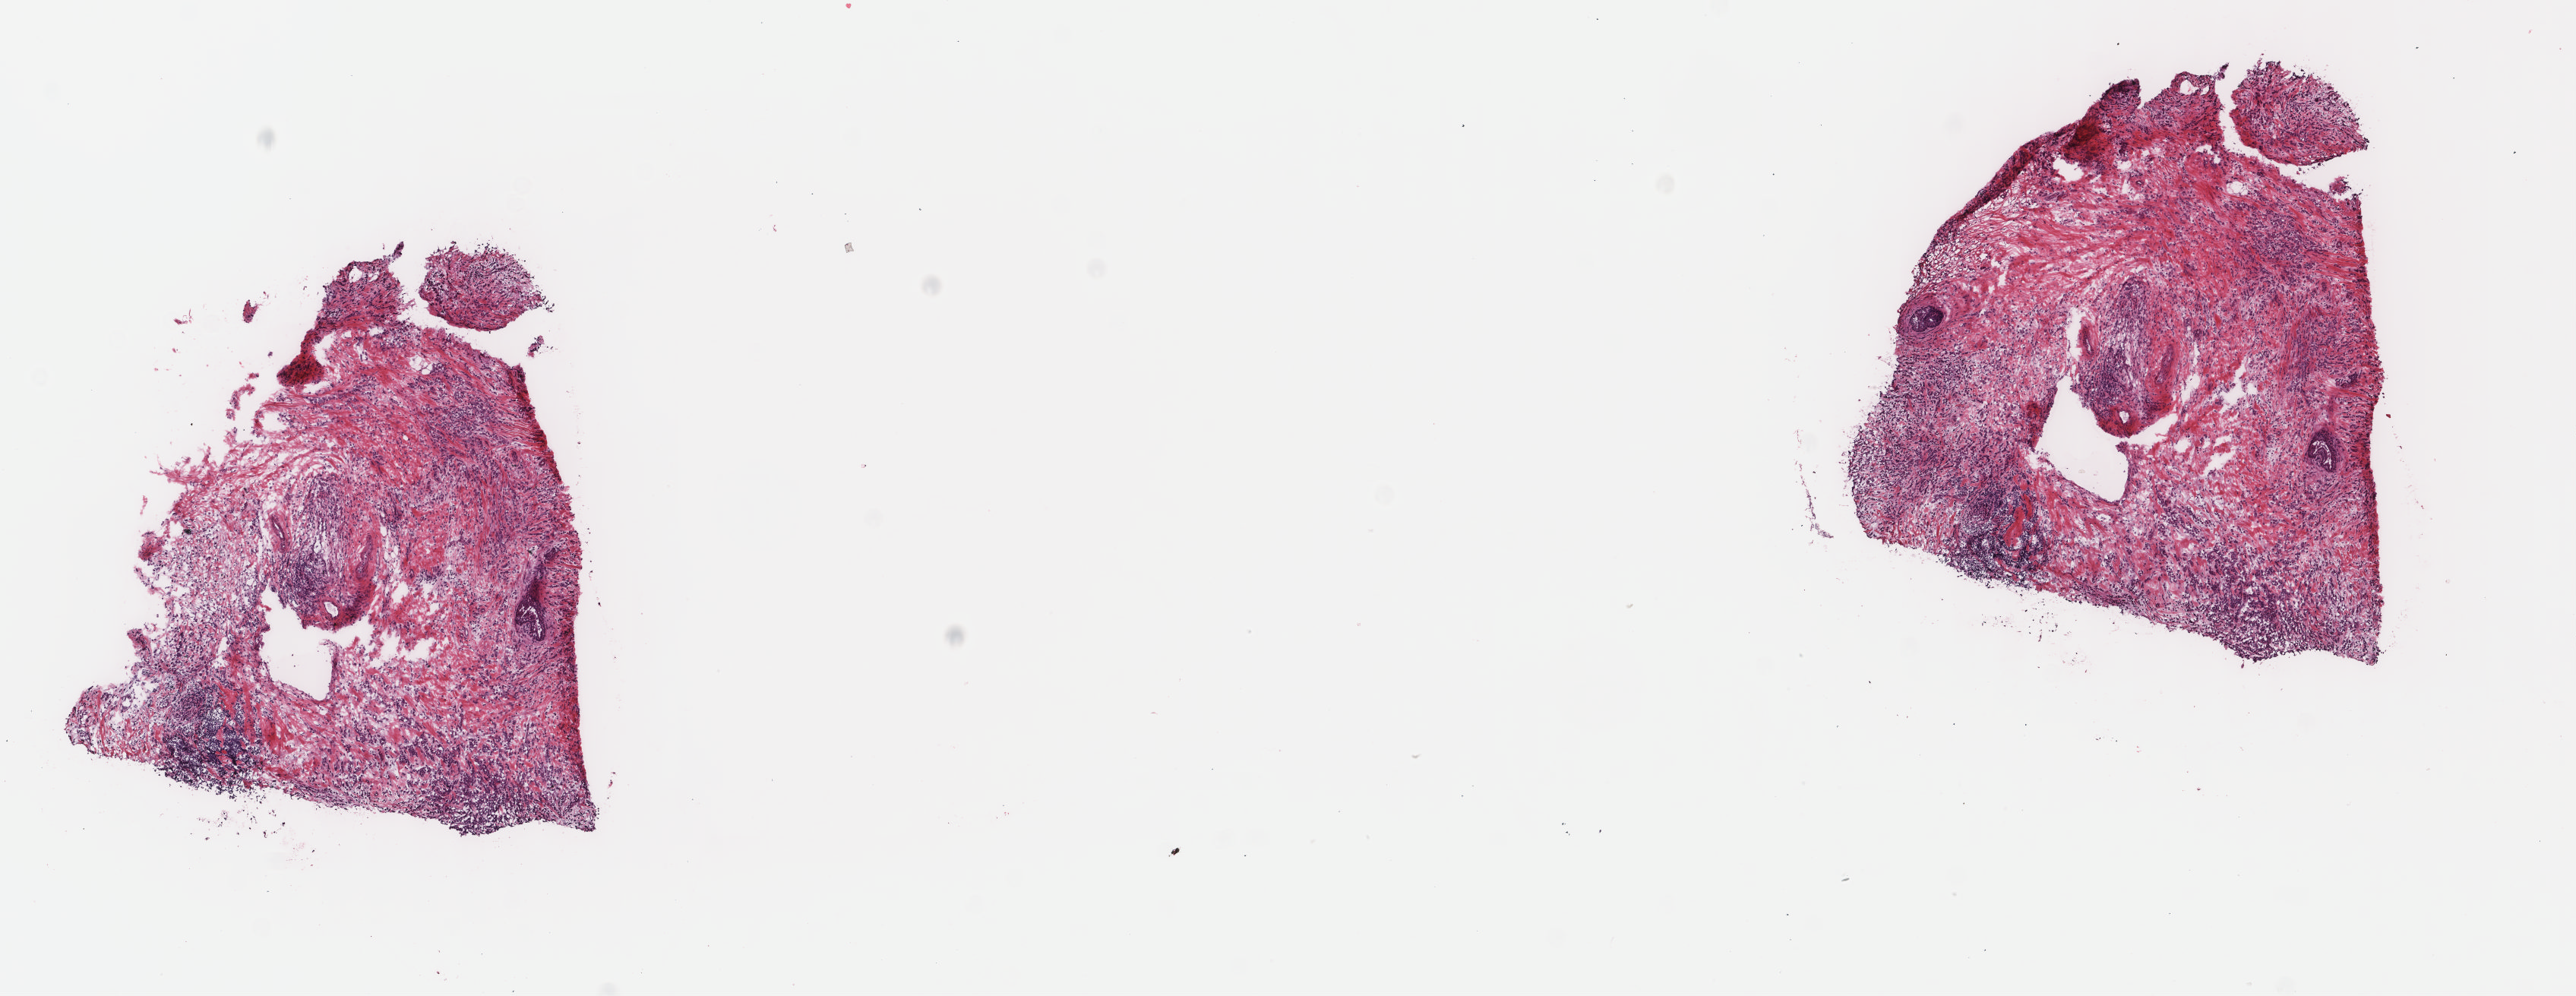
Whole-slide histology image, H&E — a low-resolution overview of the entire scanned area, about 13.5 x 5.2 mm (from a 40x scan), frozen section from the top of the tissue portion, primary tumour sample from the breast. Patient: female, age at initial diagnosis 46 years. Slide review estimates, as recorded: tumour cells 50%, tumour nuclei 85%, normal cells 0%, stromal cells 50%, necrosis 0%. Inflammatory infiltration, as recorded: lymphocyte infiltration 3%, monocyte infiltration 1%, neutrophil infiltration 1%.
AJCC pathologic stage: IIB. Diagnosis: Lobular carcinoma, NOS. Lymph nodes positive (case pathology): 1 of 16 examined. TNM: T2 N1 M0. Laterality: left.